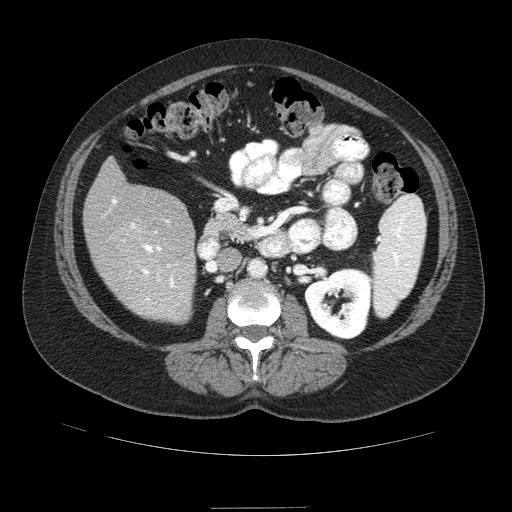
Contrast-enhanced abdominal CT (liver protocol), one axial slice. Reconstruction kernel STANDARD. Soft-tissue window (W 400 / L 40 HU). 512 × 512 image matrix. Case-level facts recorded for this patient, not image findings: diagnosis: hepatocellular carcinoma (patient treated with transarterial chemoembolisation; whether this scan precedes or follows treatment is not stated here); TNM stage (as recorded): Stage-IIIB; Child-Pugh class: A.
Outlined on this slice (semi-automatic segmentation, software-assisted and operator-edited):
- liver parenchyma outside the tumour (the mass and vessels are separate outlines, so this box may not span the whole liver): bounding box (x1, y1, x2, y2) in pixels: (84, 156, 196, 321)
- liver vessels: (112, 199, 175, 301)